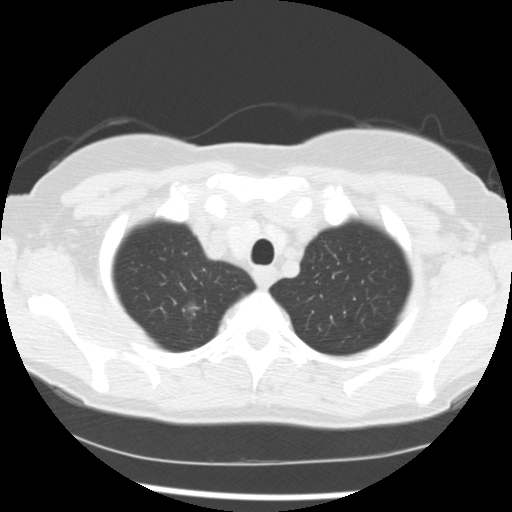
Low-dose screening chest CT, axial slice; first (baseline) screen; lung window (W 1500 / L -600 HU); 2.5 mm slice thickness; standard (soft-tissue) reconstruction kernel (STANDARD); slice 25 of 241 in the series. Female, age 60 years at enrolment. Former smoker at enrolment.
Lesion marked by an expert reader, bounding box (x1, y1, x2, y2) in pixels: (166, 290, 213, 332). The screening reader recorded 3 non-calcified nodules or masses ≥4 mm on this exam; which of them this box marks is not recorded. Lung cancer was diagnosed 100 days after this screen: bronchiolo-alveolar adenocarcinoma, NOS, right upper lobe, moderately differentiated (G2), stage IA (AJCC 6th edition), 9 mm at pathology.